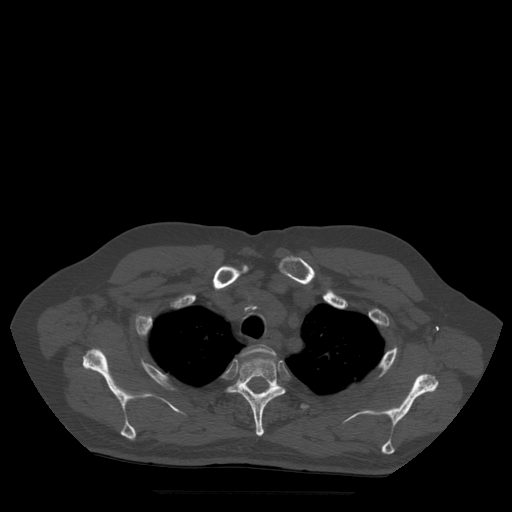
CT including the spine, one axial slice; position 409 of 522 along the scan axis; bone window (W 1800 / L 400 HU); 1.25 mm slice thickness; 512 × 512 image matrix. Patient age 72 years. From the clinical record (not read from this slice): primary cancer: prostate.
Structures marked on this image (semi-automatically segmented with operator editing):
- T2 vertebra: bounding box <242,345,276,361> (left, top, right, bottom; pixels)
- T3 vertebra: <228,358,286,436>